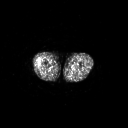
FDG PET of an extremity soft-tissue mass (from a PET/CT study), one axial slice; position 217 of 267 along the scan axis; 128 × 128 image matrix, field of view 700 × 700 mm. Patient: male, 43 years. Case-level facts recorded for this patient, not image findings: histological type: poorly differentiated synovial sarcoma; grade: high; site of the primary tumour: right buttock.
Annotated regions visible in this slice (expert contour drawn on MRI and transferred to this co-registered scan by the dataset authors):
- gross tumour volume including surrounding oedema: bounding box <37,60,42,66> (left, top, right, bottom; pixels)